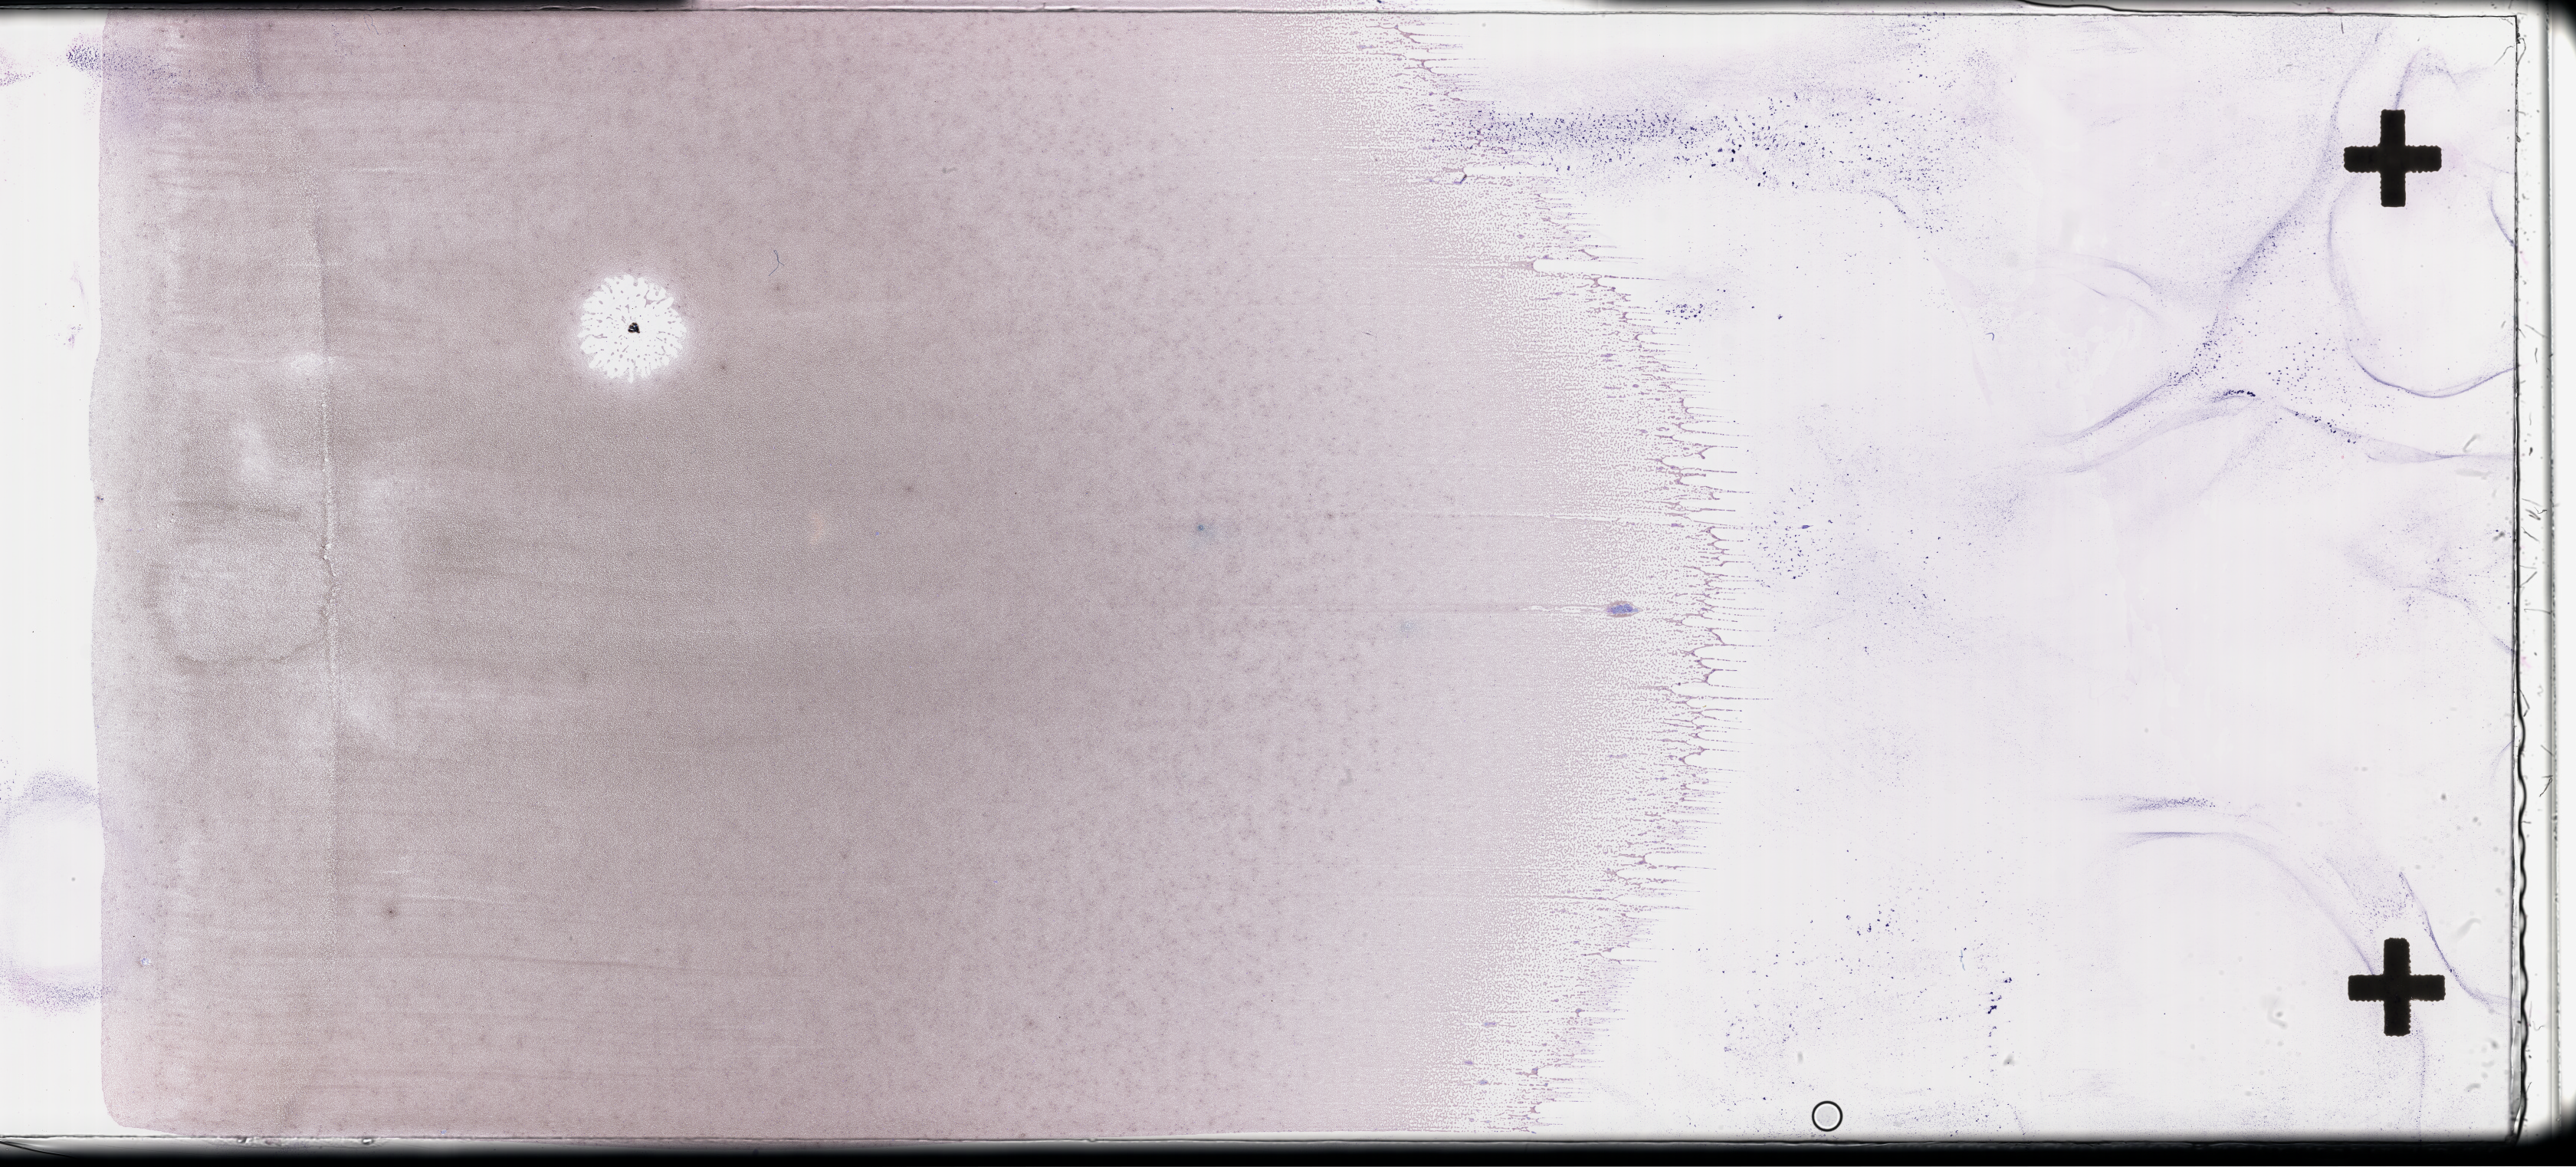
Wright-Giemsa-stained whole blood smear, whole-slide image, shown as a low-resolution overview of the whole scanned area (about 54.3 x 24.6 mm). Patient sex: male.
• patient diagnosis: Plasma Cell Myeloma